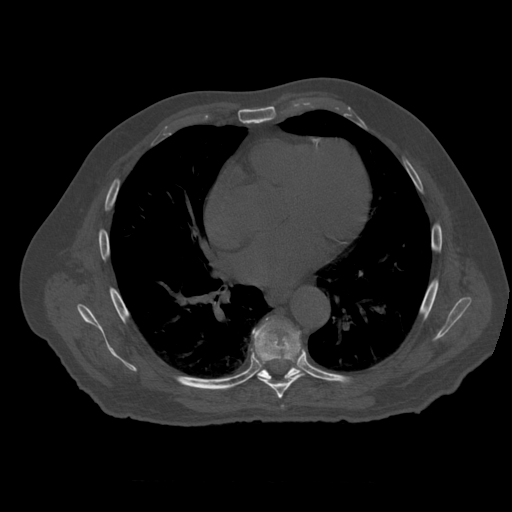
CT including the spine, one axial slice; slice 353 of 399 in the series (ordered by position); 120 kVp; bone window (W 1800 / L 400 HU); 1.25 mm slice thickness; 512 × 512 image matrix. Patient age 73 years. Case-level facts recorded for this patient, not image findings: primary cancer: prostate.
Outlined on this slice (semi-automatically segmented with operator editing):
- T7 vertebra: bounding box (x1, y1, x2, y2) in pixels: (253, 319, 305, 399)
- T8 vertebra: (259, 342, 300, 380)